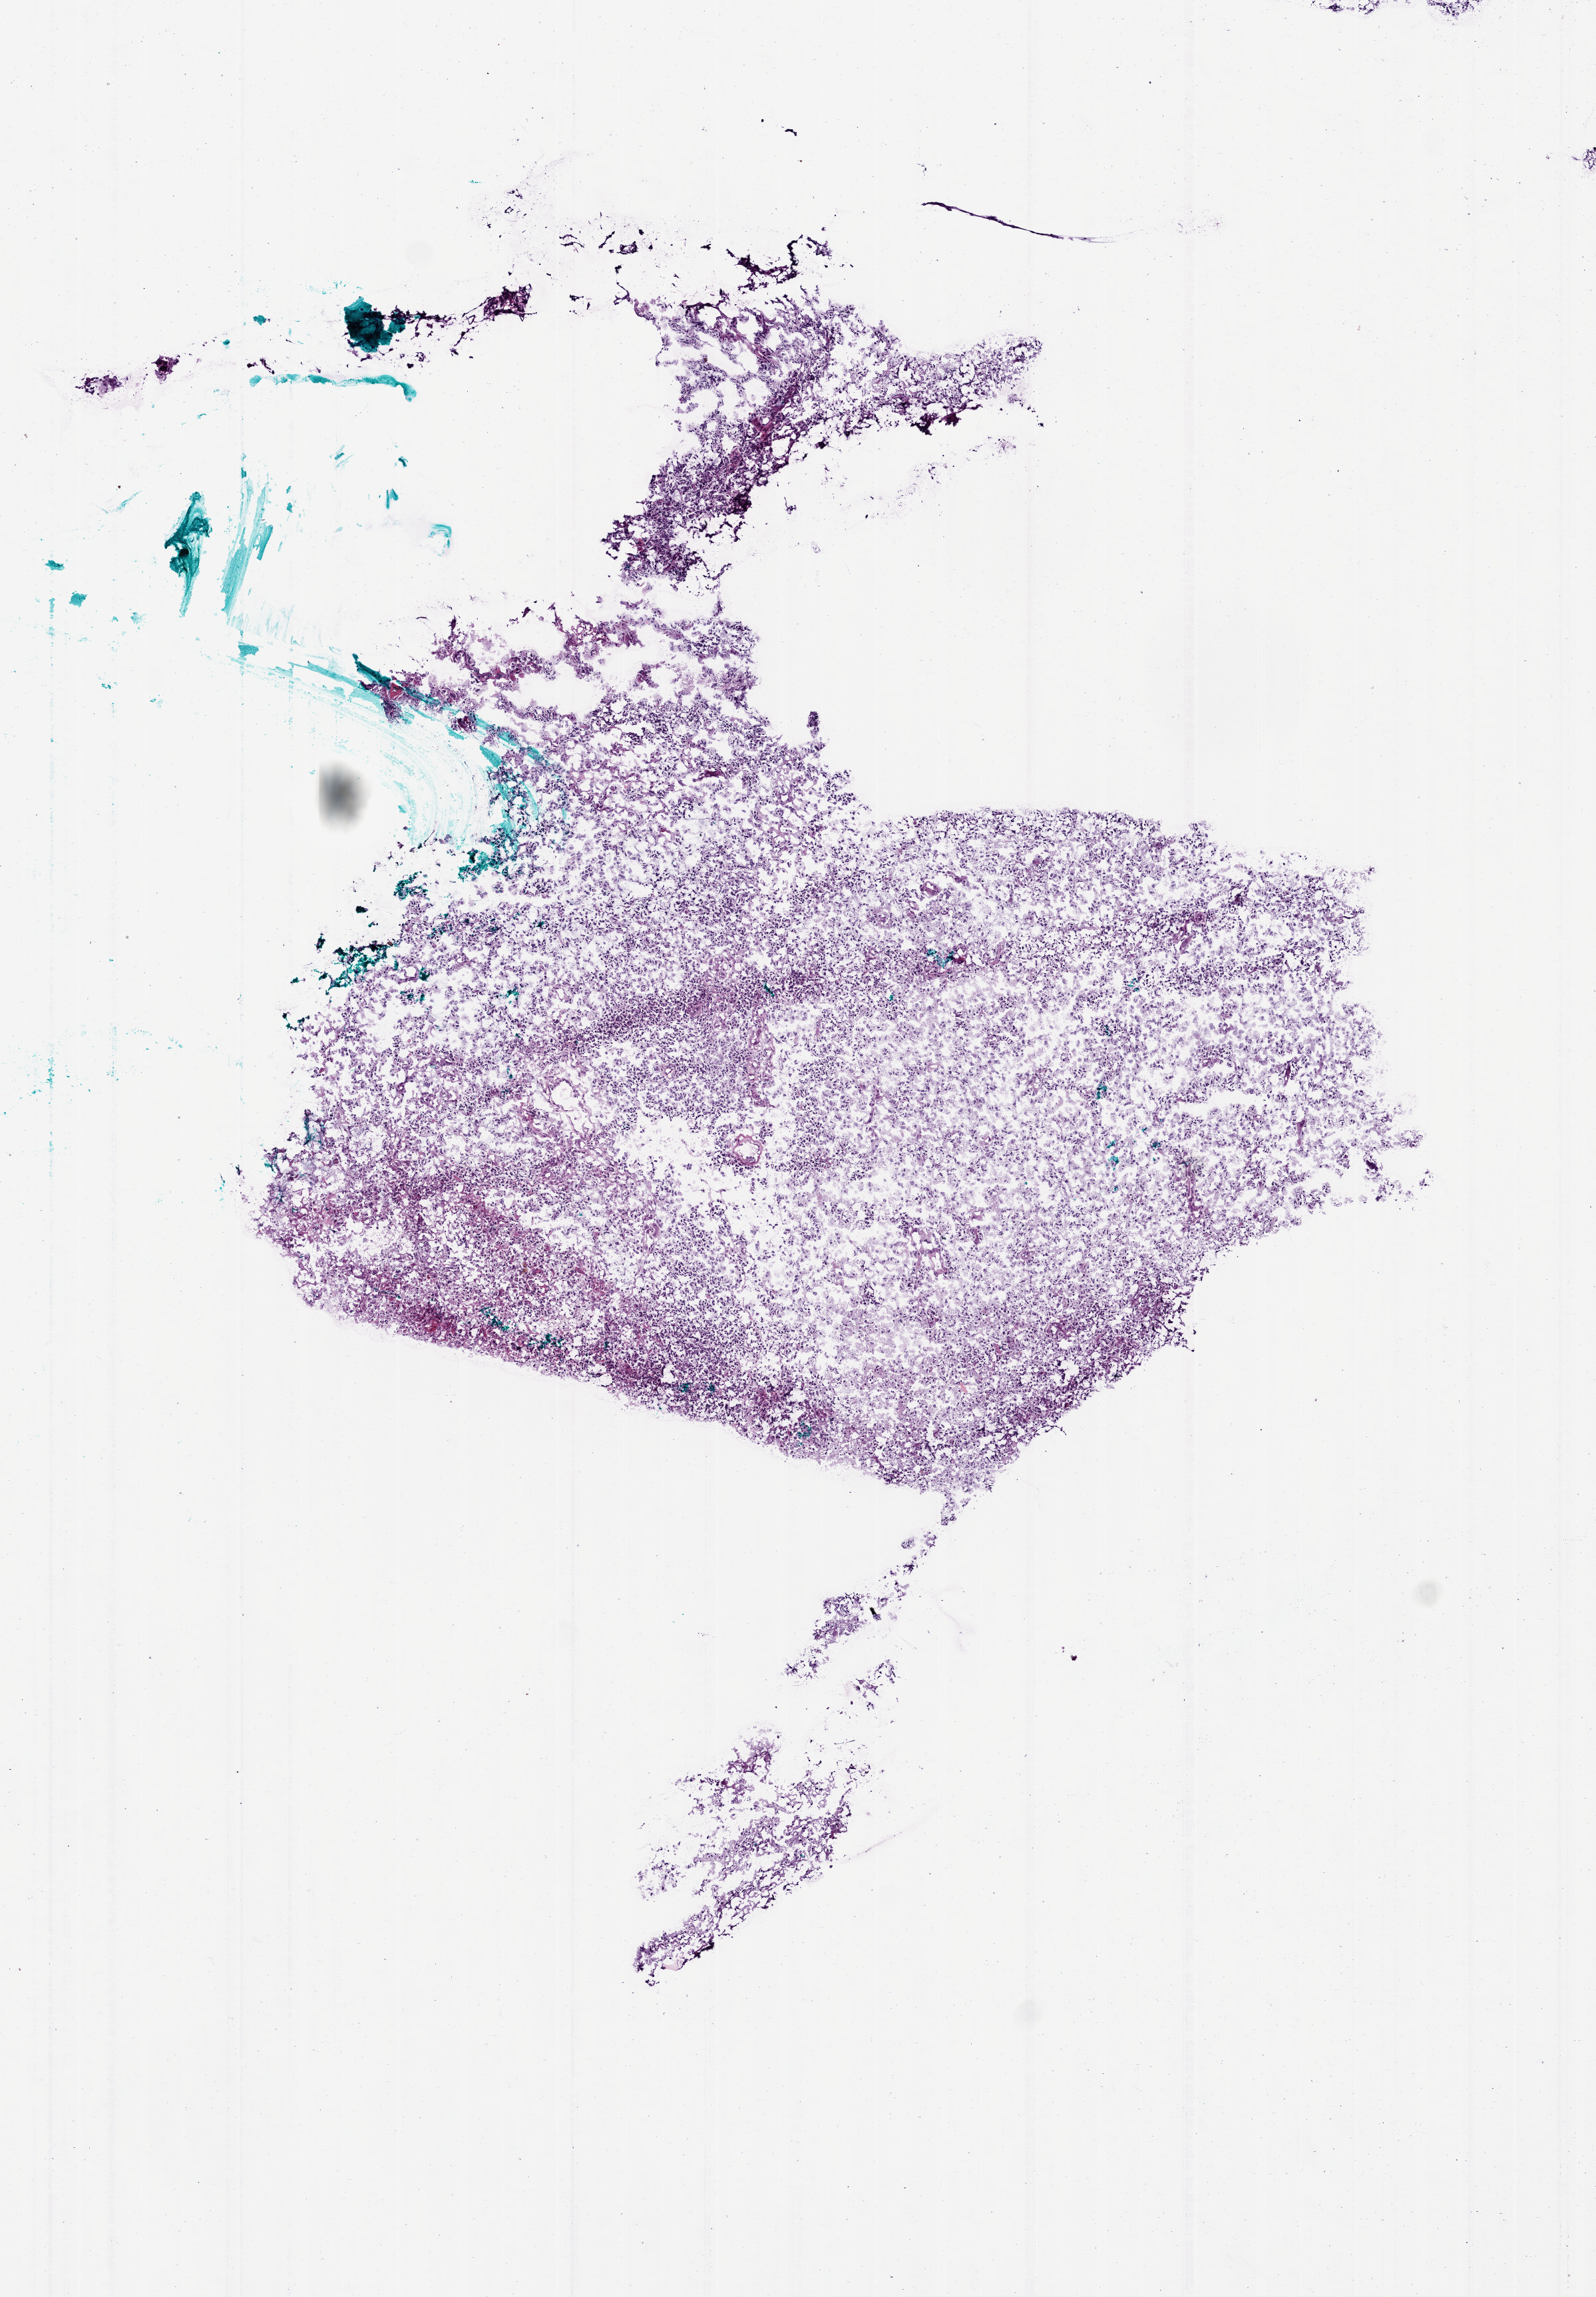
H&E-stained whole-slide image — whole scanned area (about 4.8 x 7.0 mm) shown as a low-resolution overview; frozen section from the bottom of the tissue portion; sample: primary tumour, brain. Female patient; age at initial diagnosis 77 years. Pathologist review of this section (percent, as recorded): tumour cells 90%, tumour nuclei 90%, normal cells 0%, stromal cells 5%, necrosis 5%.
Diagnosis: Glioblastoma.